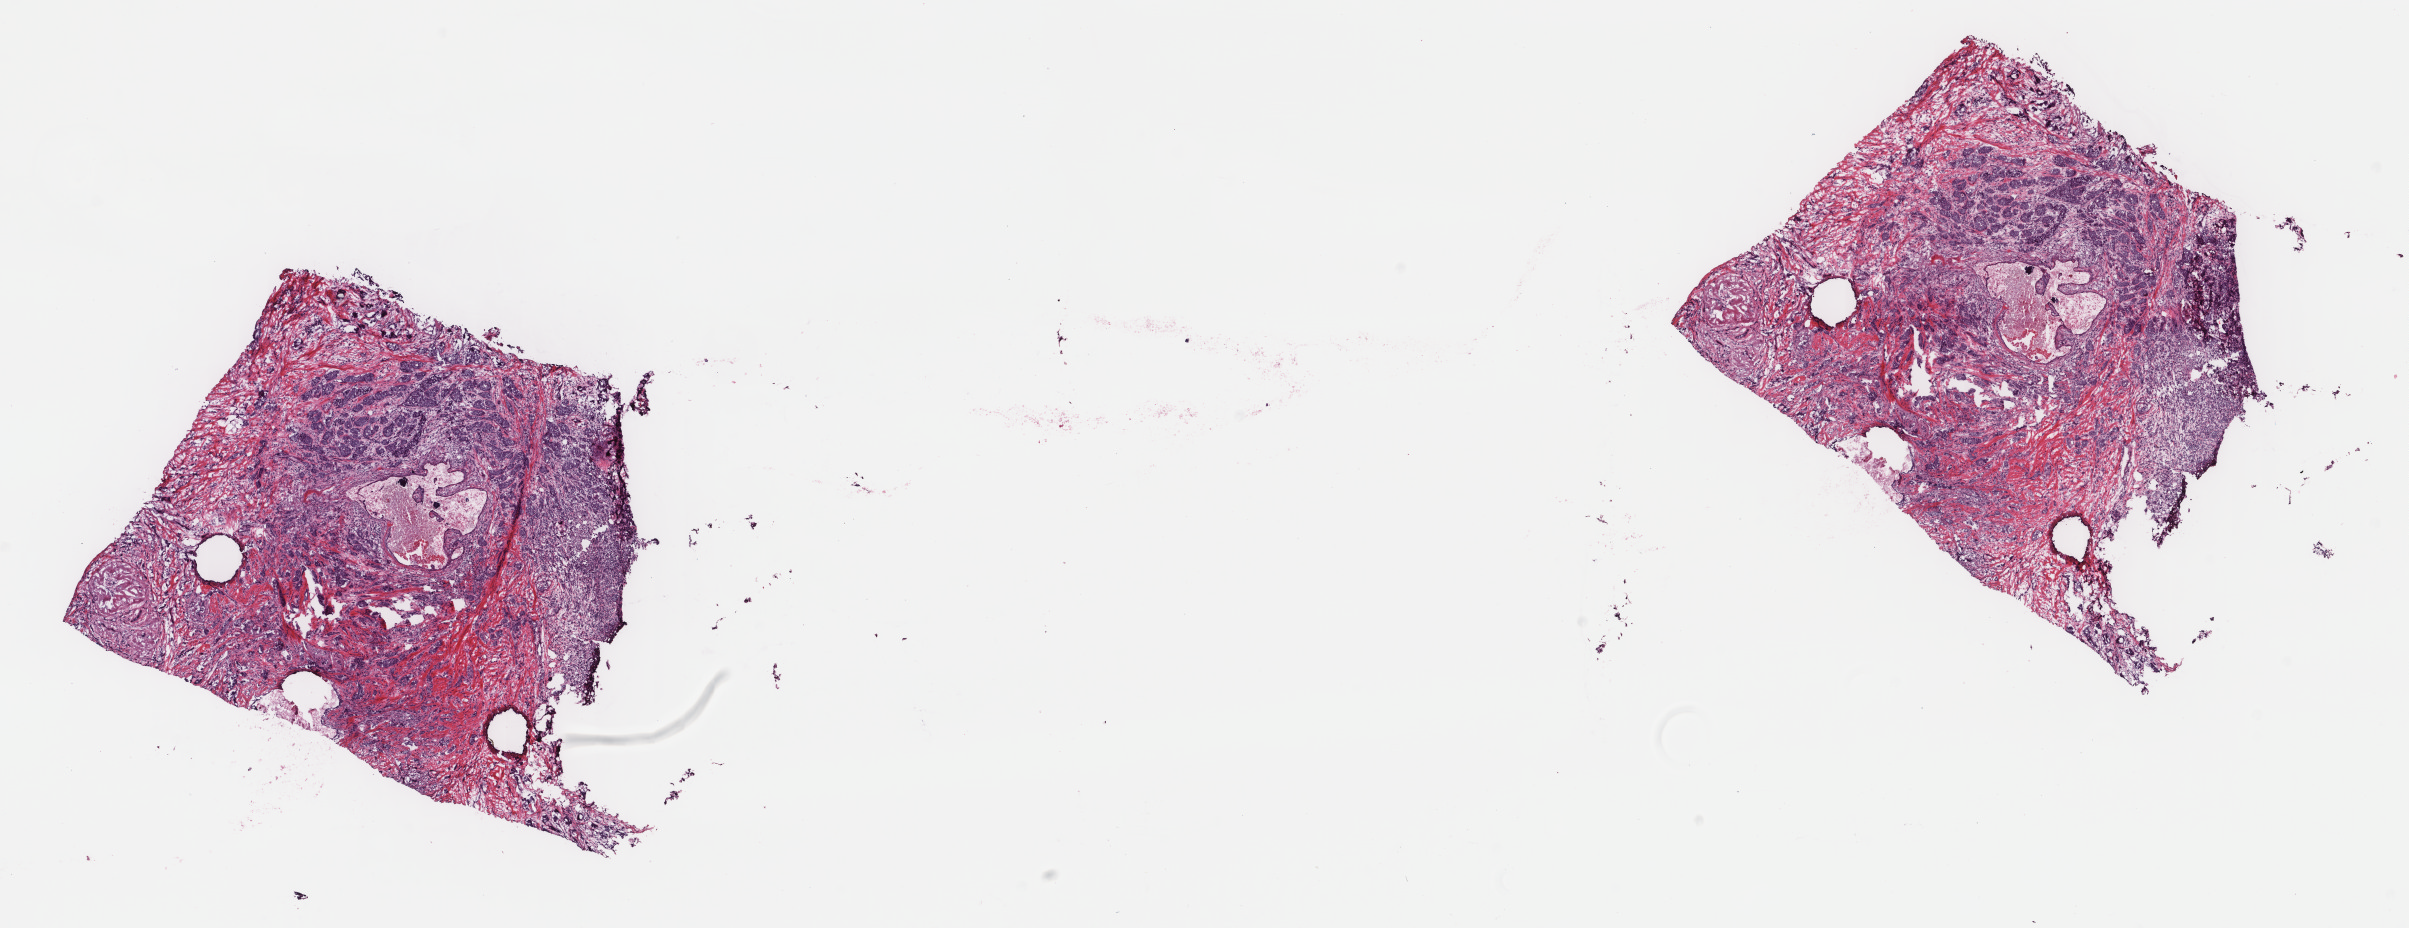
Digitized H&E tissue section (whole slide) — a low-resolution overview of the entire scanned area, about 19.1 x 7.4 mm. Frozen section from the top of the tissue portion. Sample: primary tumour, breast. Female, age 62 years at initial diagnosis. Slide review estimates, as recorded: tumour cells 65%, tumour nuclei 85%, normal cells 0%, stromal cells 30%, necrosis 5%. Inflammatory infiltration, as recorded: lymphocyte infiltration 1%, monocyte infiltration 0%, neutrophil infiltration 0%.
- lymph nodes positive (case pathology): 1 of 1 examined
- AJCC pathologic stage: IIB
- laterality: left
- pathologic diagnosis: Infiltrating duct carcinoma, NOS